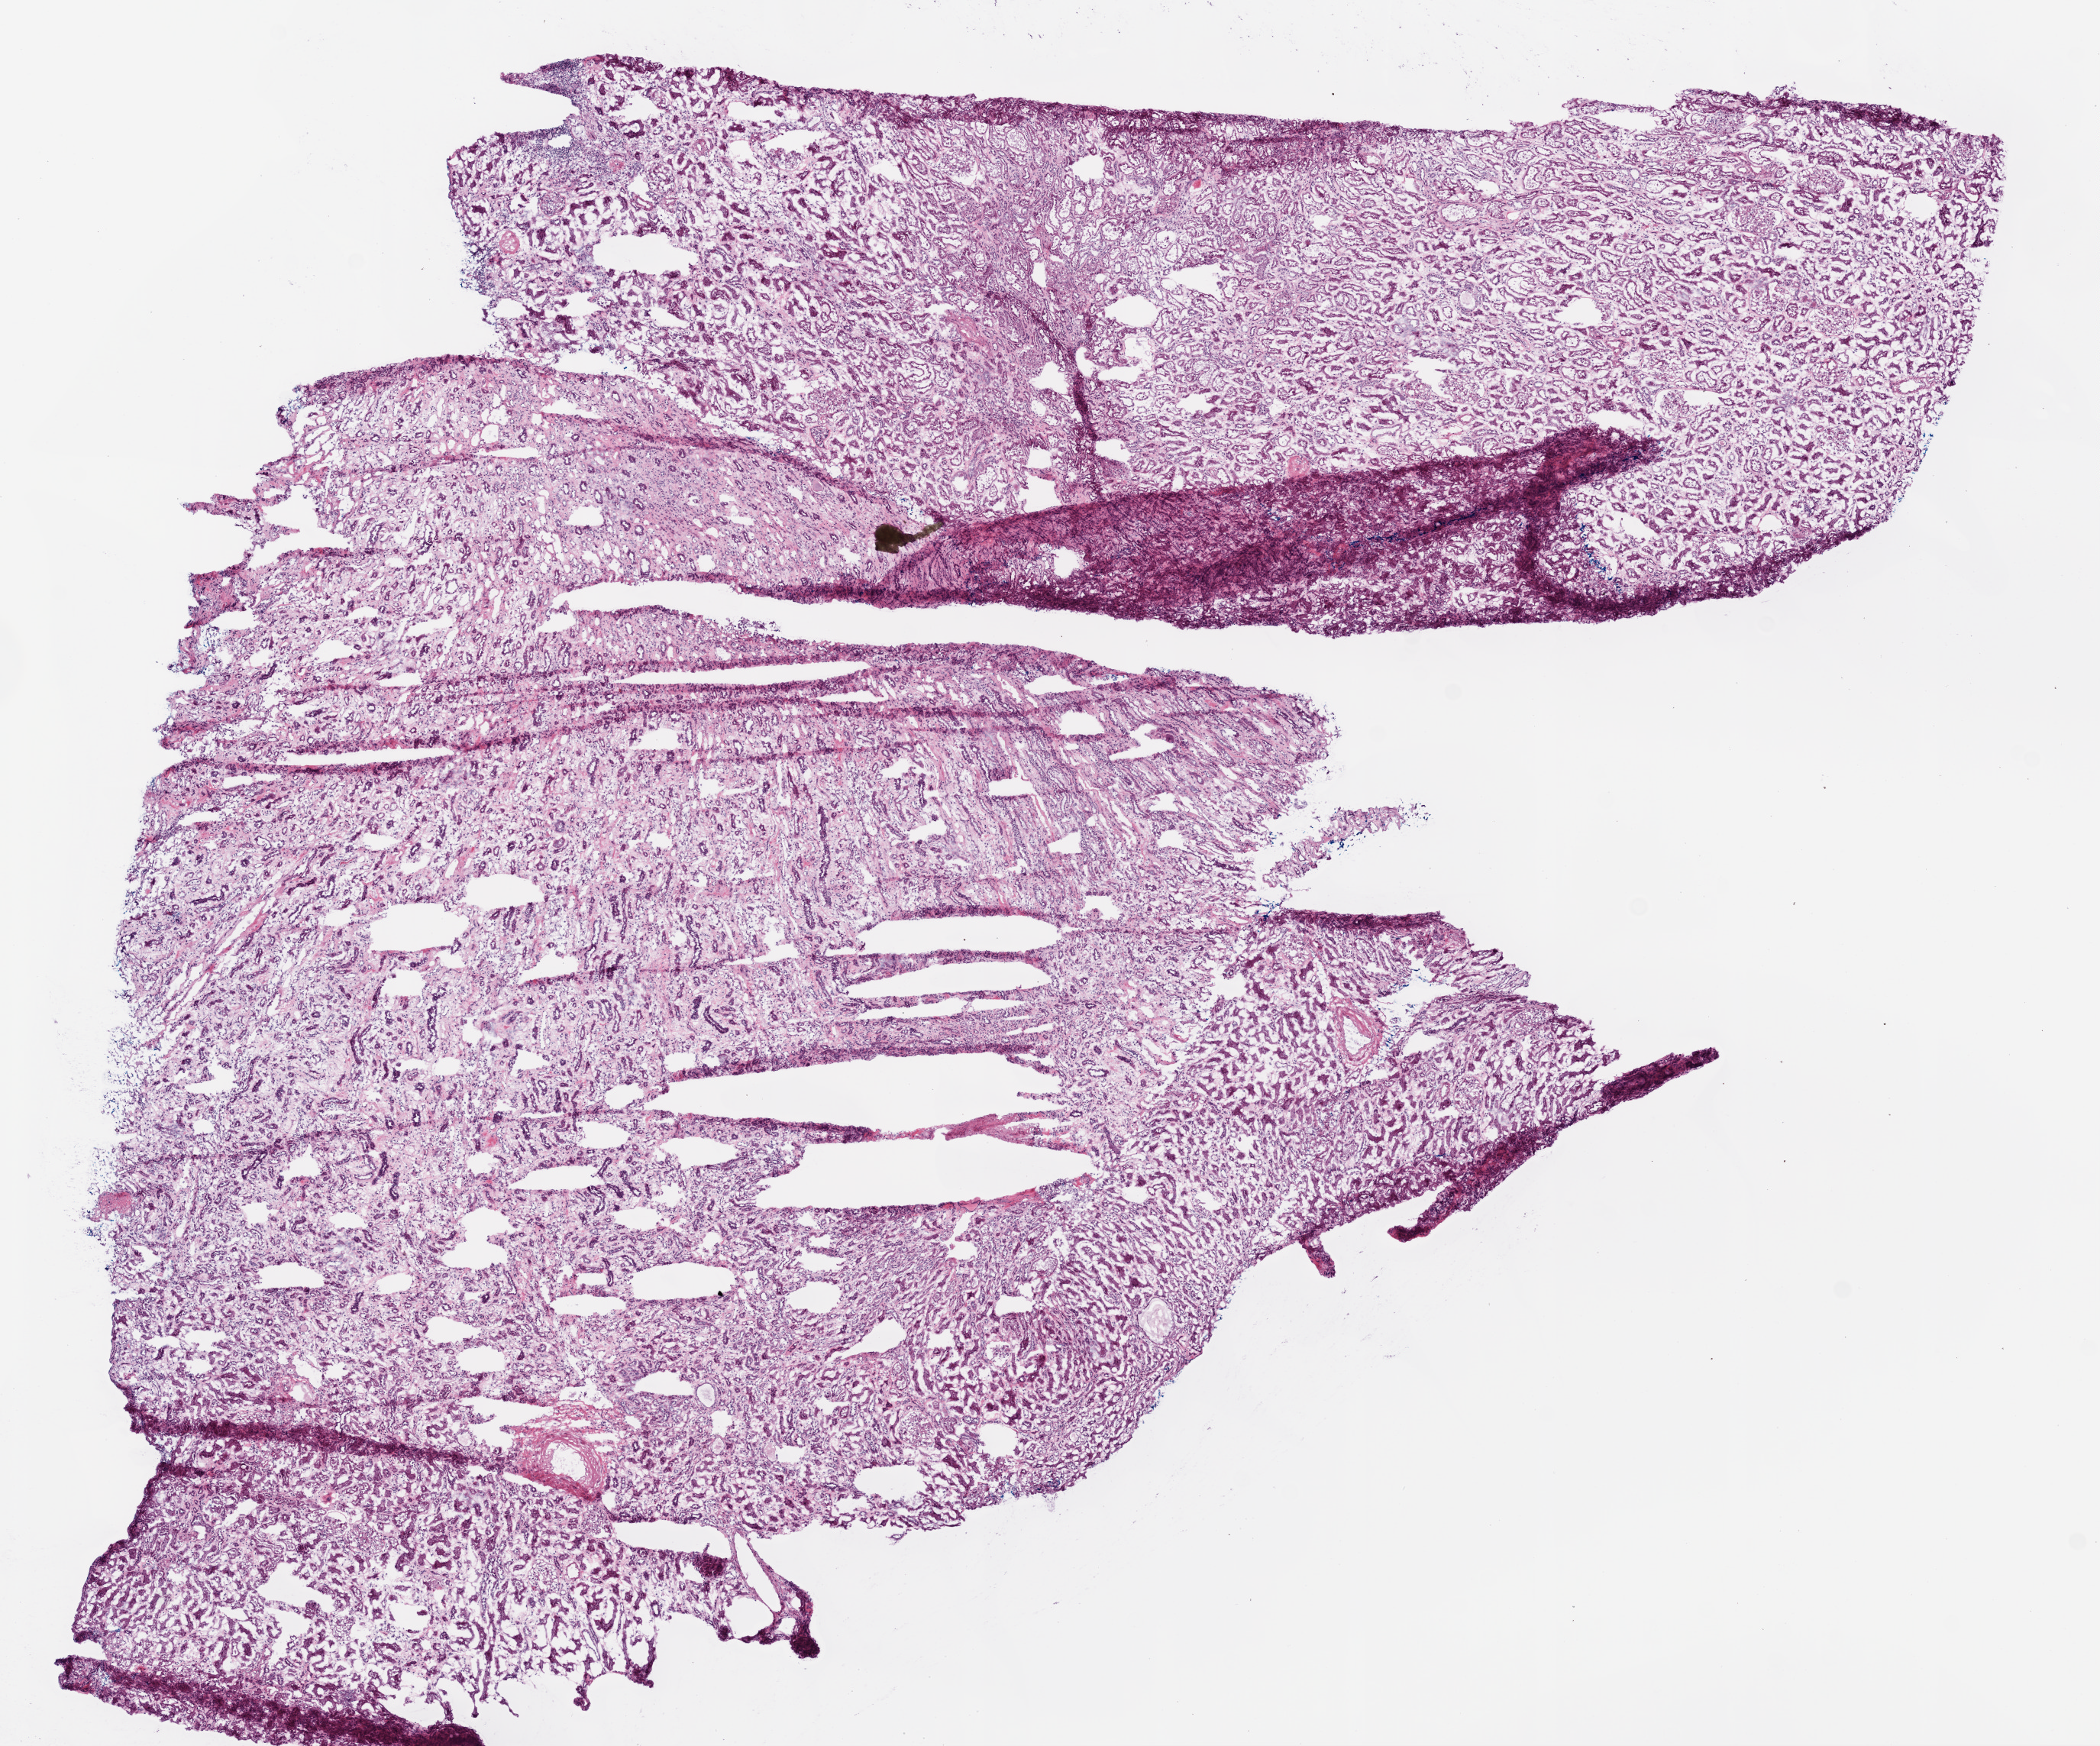
Whole-slide histology image, H&E-stained, a low-resolution overview of the entire scanned area, about 11.0 x 9.2 mm; frozen section from the top of the tissue portion; solid tissue normal (non-tumour tissue) sample from the kidney. Female, age 75 years at initial diagnosis.
This section: solid tissue normal sample (biorepository sample class). Patient diagnosis: Clear cell adenocarcinoma, NOS.